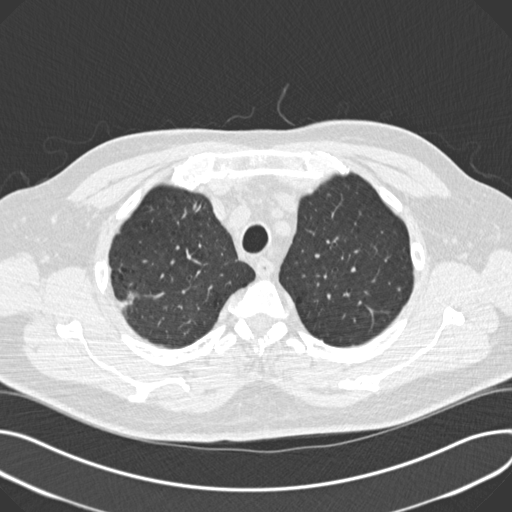
Low-dose screening chest CT, one axial slice. Slice 149 of 180 in the series (ordered by position). Reconstruction kernel B30f. 120 kVp. Lung window (W 1500 / L -600 HU). 2 mm slice thickness. 512 × 512 image matrix, field of view 376 × 376 mm.
Outlined on this slice (manually delineated by an expert):
- lesion 2 (tumor, upper lobe of right lung): box from (x=193, y=200) to (x=202, y=212) px